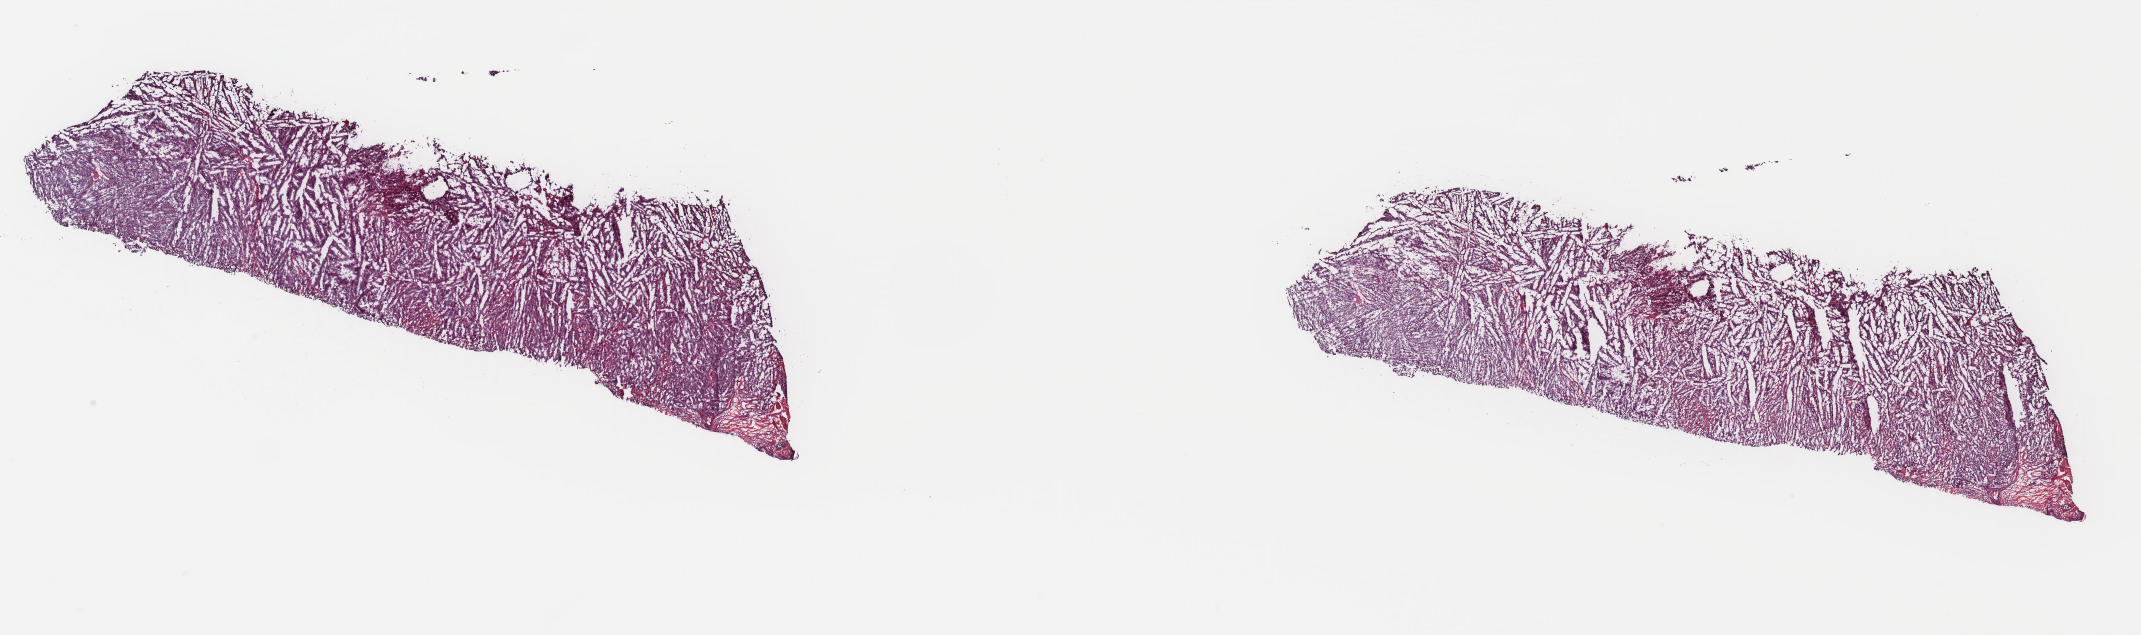
Digitized H&E-stained tissue section (whole slide) — a low-resolution overview of the entire scanned area, about 34.0 x 10.1 mm (slide scanned at 40x). Frozen section from the top of the tissue portion. Metastatic tumour sample, sampled site not recorded. Female, age 58 years at initial diagnosis. Slide review estimates, as recorded: tumour cells 90%, tumour nuclei 90%, normal cells 5%, stromal cells 3%, necrosis 2%. Infiltration values recorded for this section: lymphocyte infiltration 1%, monocyte infiltration 5%, neutrophil infiltration 0%.
This section: metastatic tumour tissue. Patient diagnosis: Malignant melanoma, NOS.